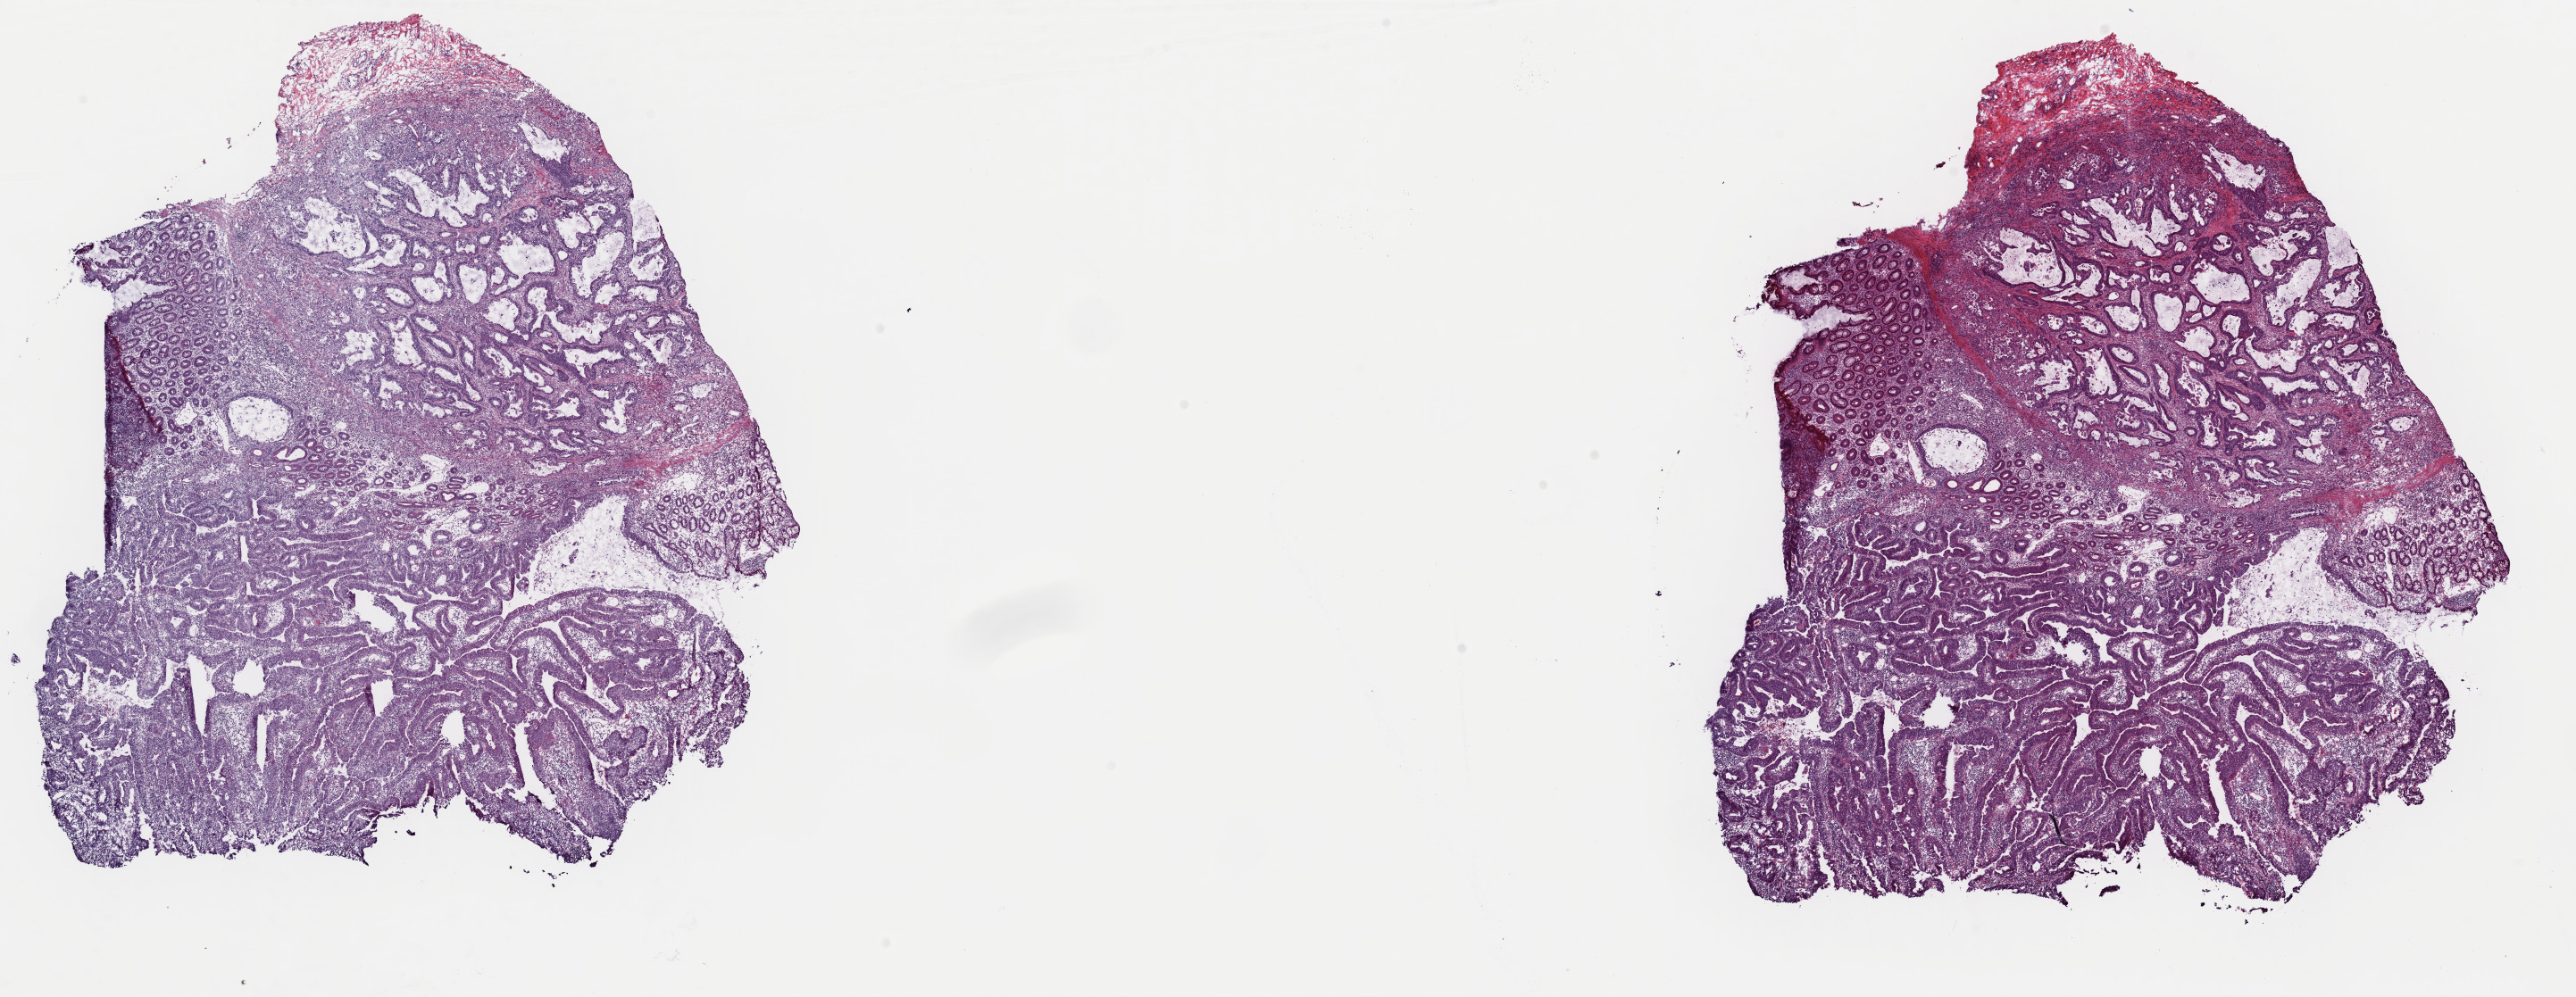
H&E-stained whole-slide image, a low-resolution overview of the entire scanned area, about 22.8 x 8.8 mm (slide scanned at 40x), frozen section from the top of the tissue portion, colon, primary tumour sample. Female patient; age at initial diagnosis 55 years. Composition of this section per pathologist review: tumour cells 65%, tumour nuclei 65%, normal cells 10%, stromal cells 25%, necrosis 0%. Infiltration values recorded for this section: lymphocyte infiltration 7%, monocyte infiltration 2%, neutrophil infiltration 4%.
- lymph nodes positive (case pathology): 11 of 15 examined
- AJCC pathologic stage: IIIC
- pathologic diagnosis: Adenocarcinoma, NOS (cecum)